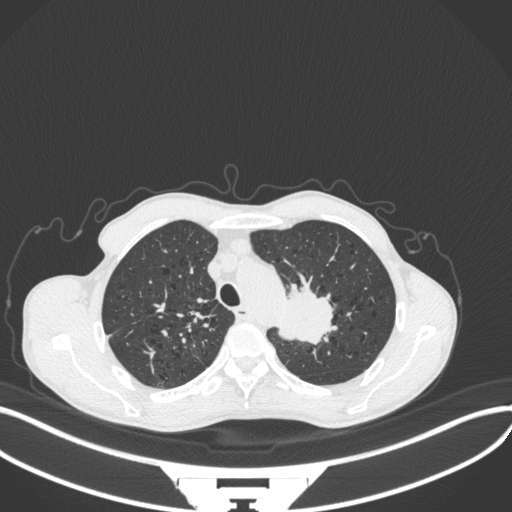
Chest CT, one axial slice; position 331 of 394 along the scan axis; reconstruction kernel B31f; 120 kVp; lung window (W 1500 / L -600 HU); 512 × 512 image matrix. Patient: male, 65 years. Case-level facts recorded for this patient, not image findings: clinical TNM (as recorded): T2b N0 M0.
Outlined on this slice (rectangle marked by the reading radiologist):
- lung tumour (recorded histology: adenocarcinoma): bounding box (x1, y1, x2, y2) in pixels: (276, 280, 336, 346)